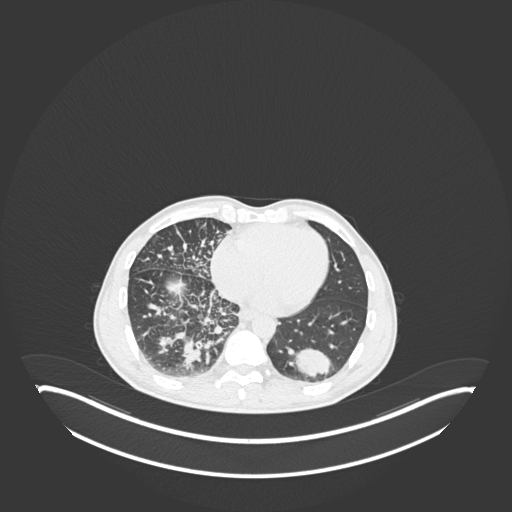
Chest CT, one axial slice. Reconstruction kernel B30f. Lung window (W 1500 / L -600 HU). 512 × 512 image matrix, field of view 500 × 500 mm. Male patient, age 49 years. Case-level facts recorded for this patient, not image findings: clinical TNM (as recorded): T2b N1 M0.
Annotated regions visible in this slice (rectangle marked by the reading radiologist):
- lung tumour (recorded histology: adenocarcinoma): bounding box <290,342,332,381> (left, top, right, bottom; pixels)